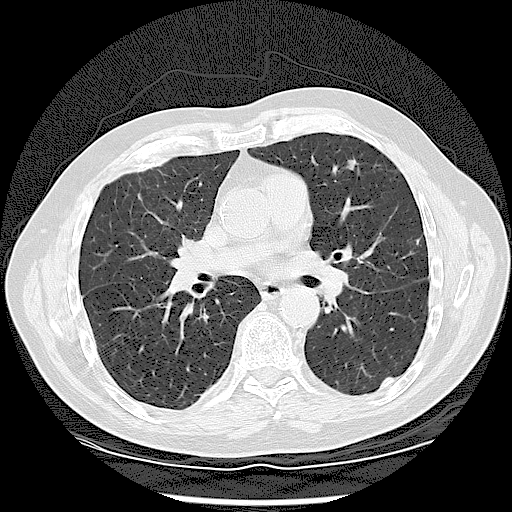
Low-dose screening chest CT, one axial slice; slice 58 of 120 in the series (ordered by position); reconstruction kernel LUNG; lung window (W 1500 / L -600 HU); 2.5 mm slice thickness; 512 × 512 image matrix.
Outlined on this slice (expert manual segmentation):
- lesion 1 (tumor, upper lobe of left lung): bounding box (x1, y1, x2, y2) in pixels: (348, 159, 357, 170)